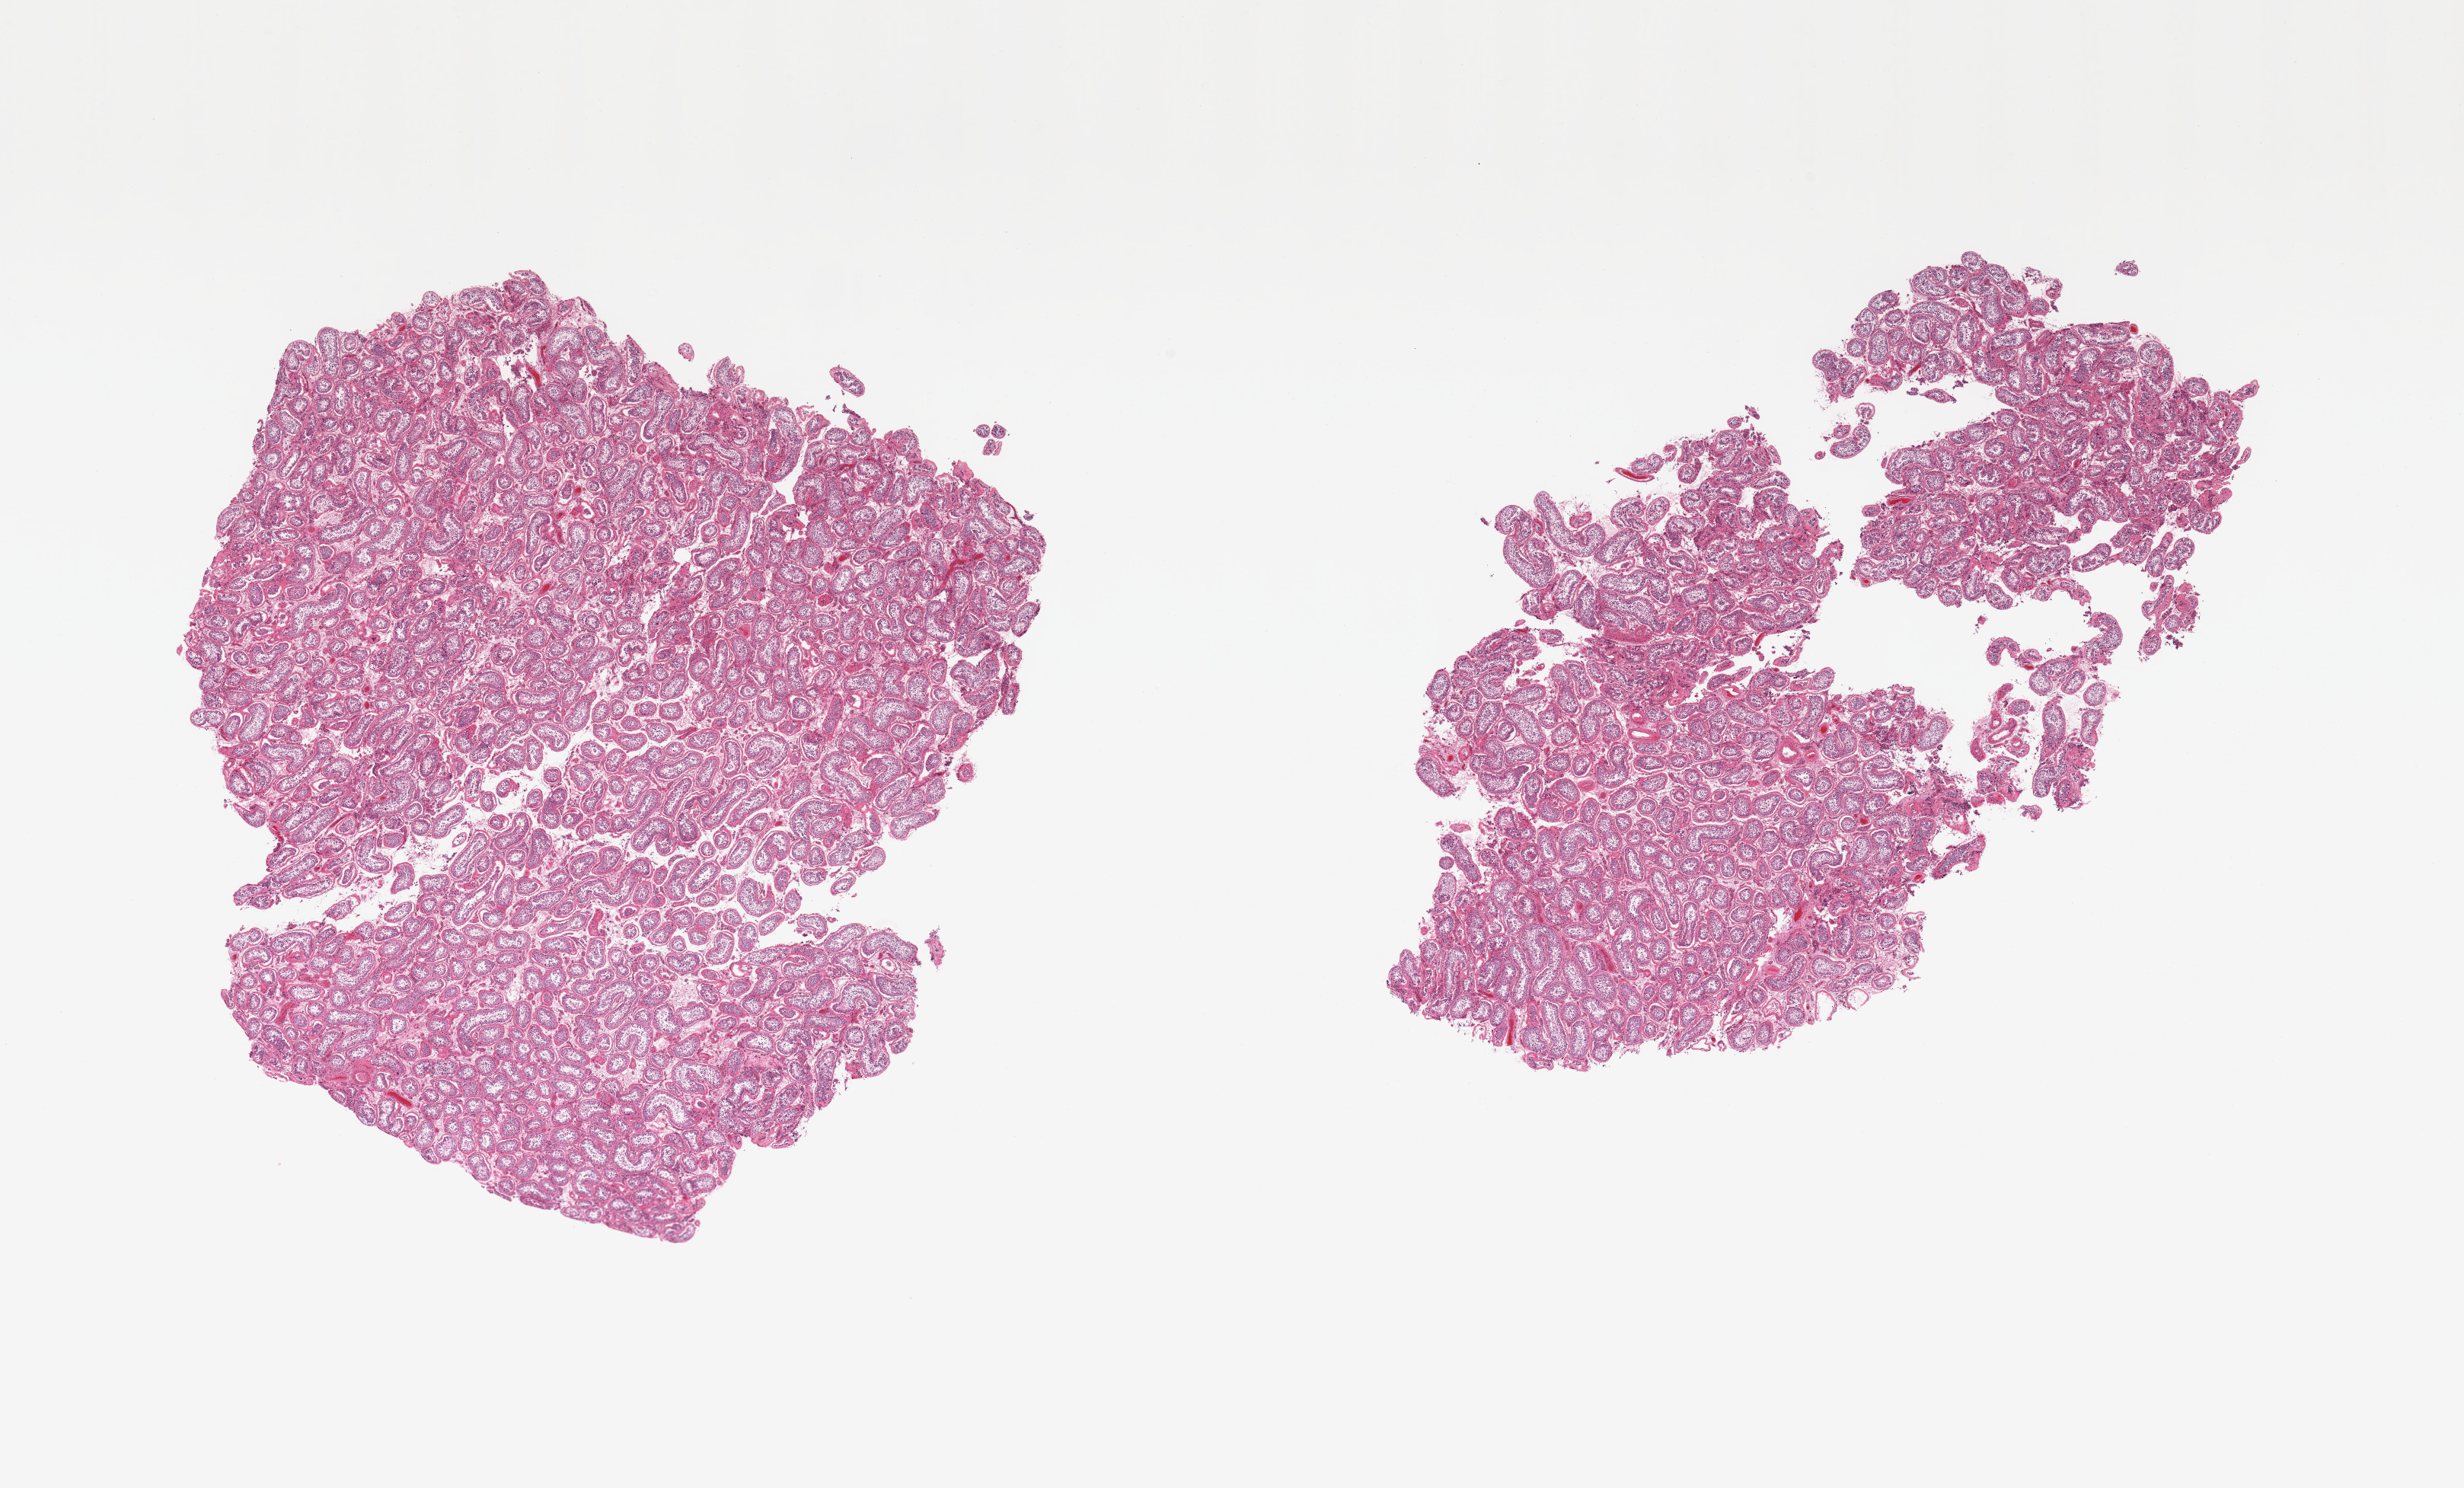
Digitized haematoxylin and eosin-stained section — low-resolution overview of the scanned area, about 25.6 x 15.5 mm (from a 20x scan). PAXgene-fixed, paraffin-embedded tissue. Section of testis (target tissue). Tissue donor sample. Donor sex: male.
Reviewer comment on this tissue sample: 2 pieces; active spermatogenesis.